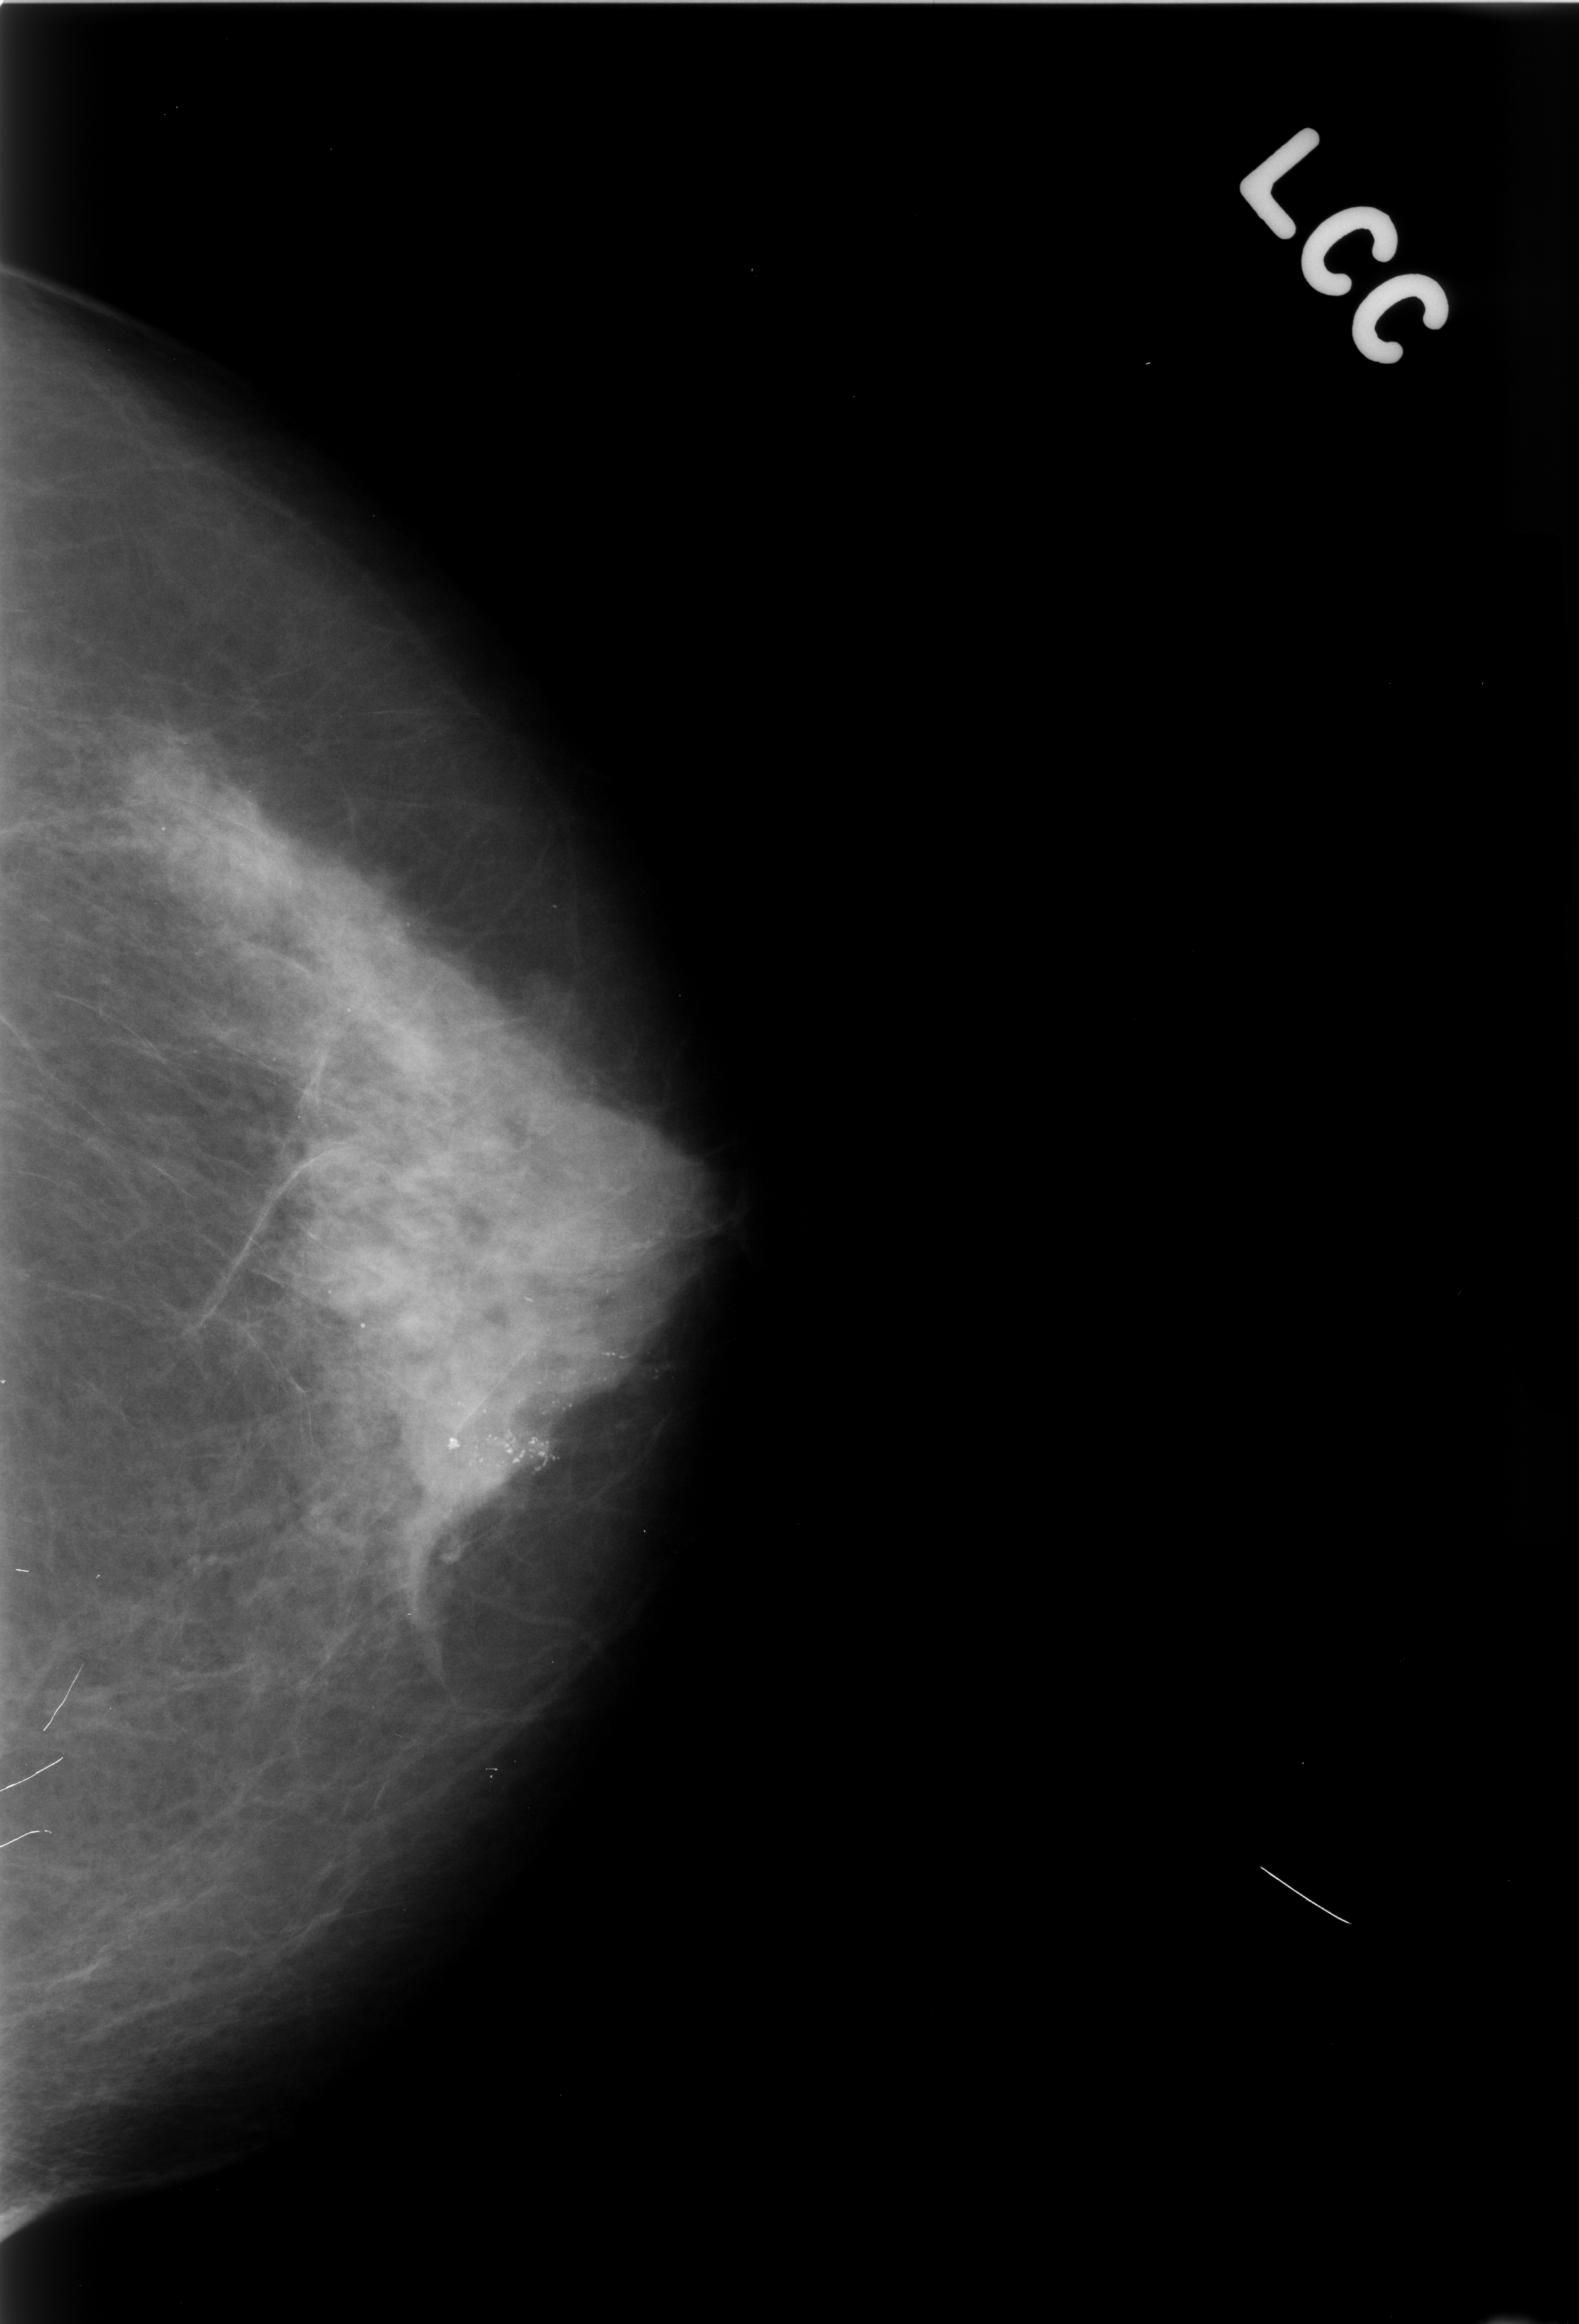
Mammogram (digitized film), left breast, craniocaudal (CC) view, BI-RADS breast density category 3 (scale 1–4).
Calcifications, morphology pleomorphic, distribution segmental; BI-RADS assessment category 5; pathology result (as recorded, not read from the image): malignant.